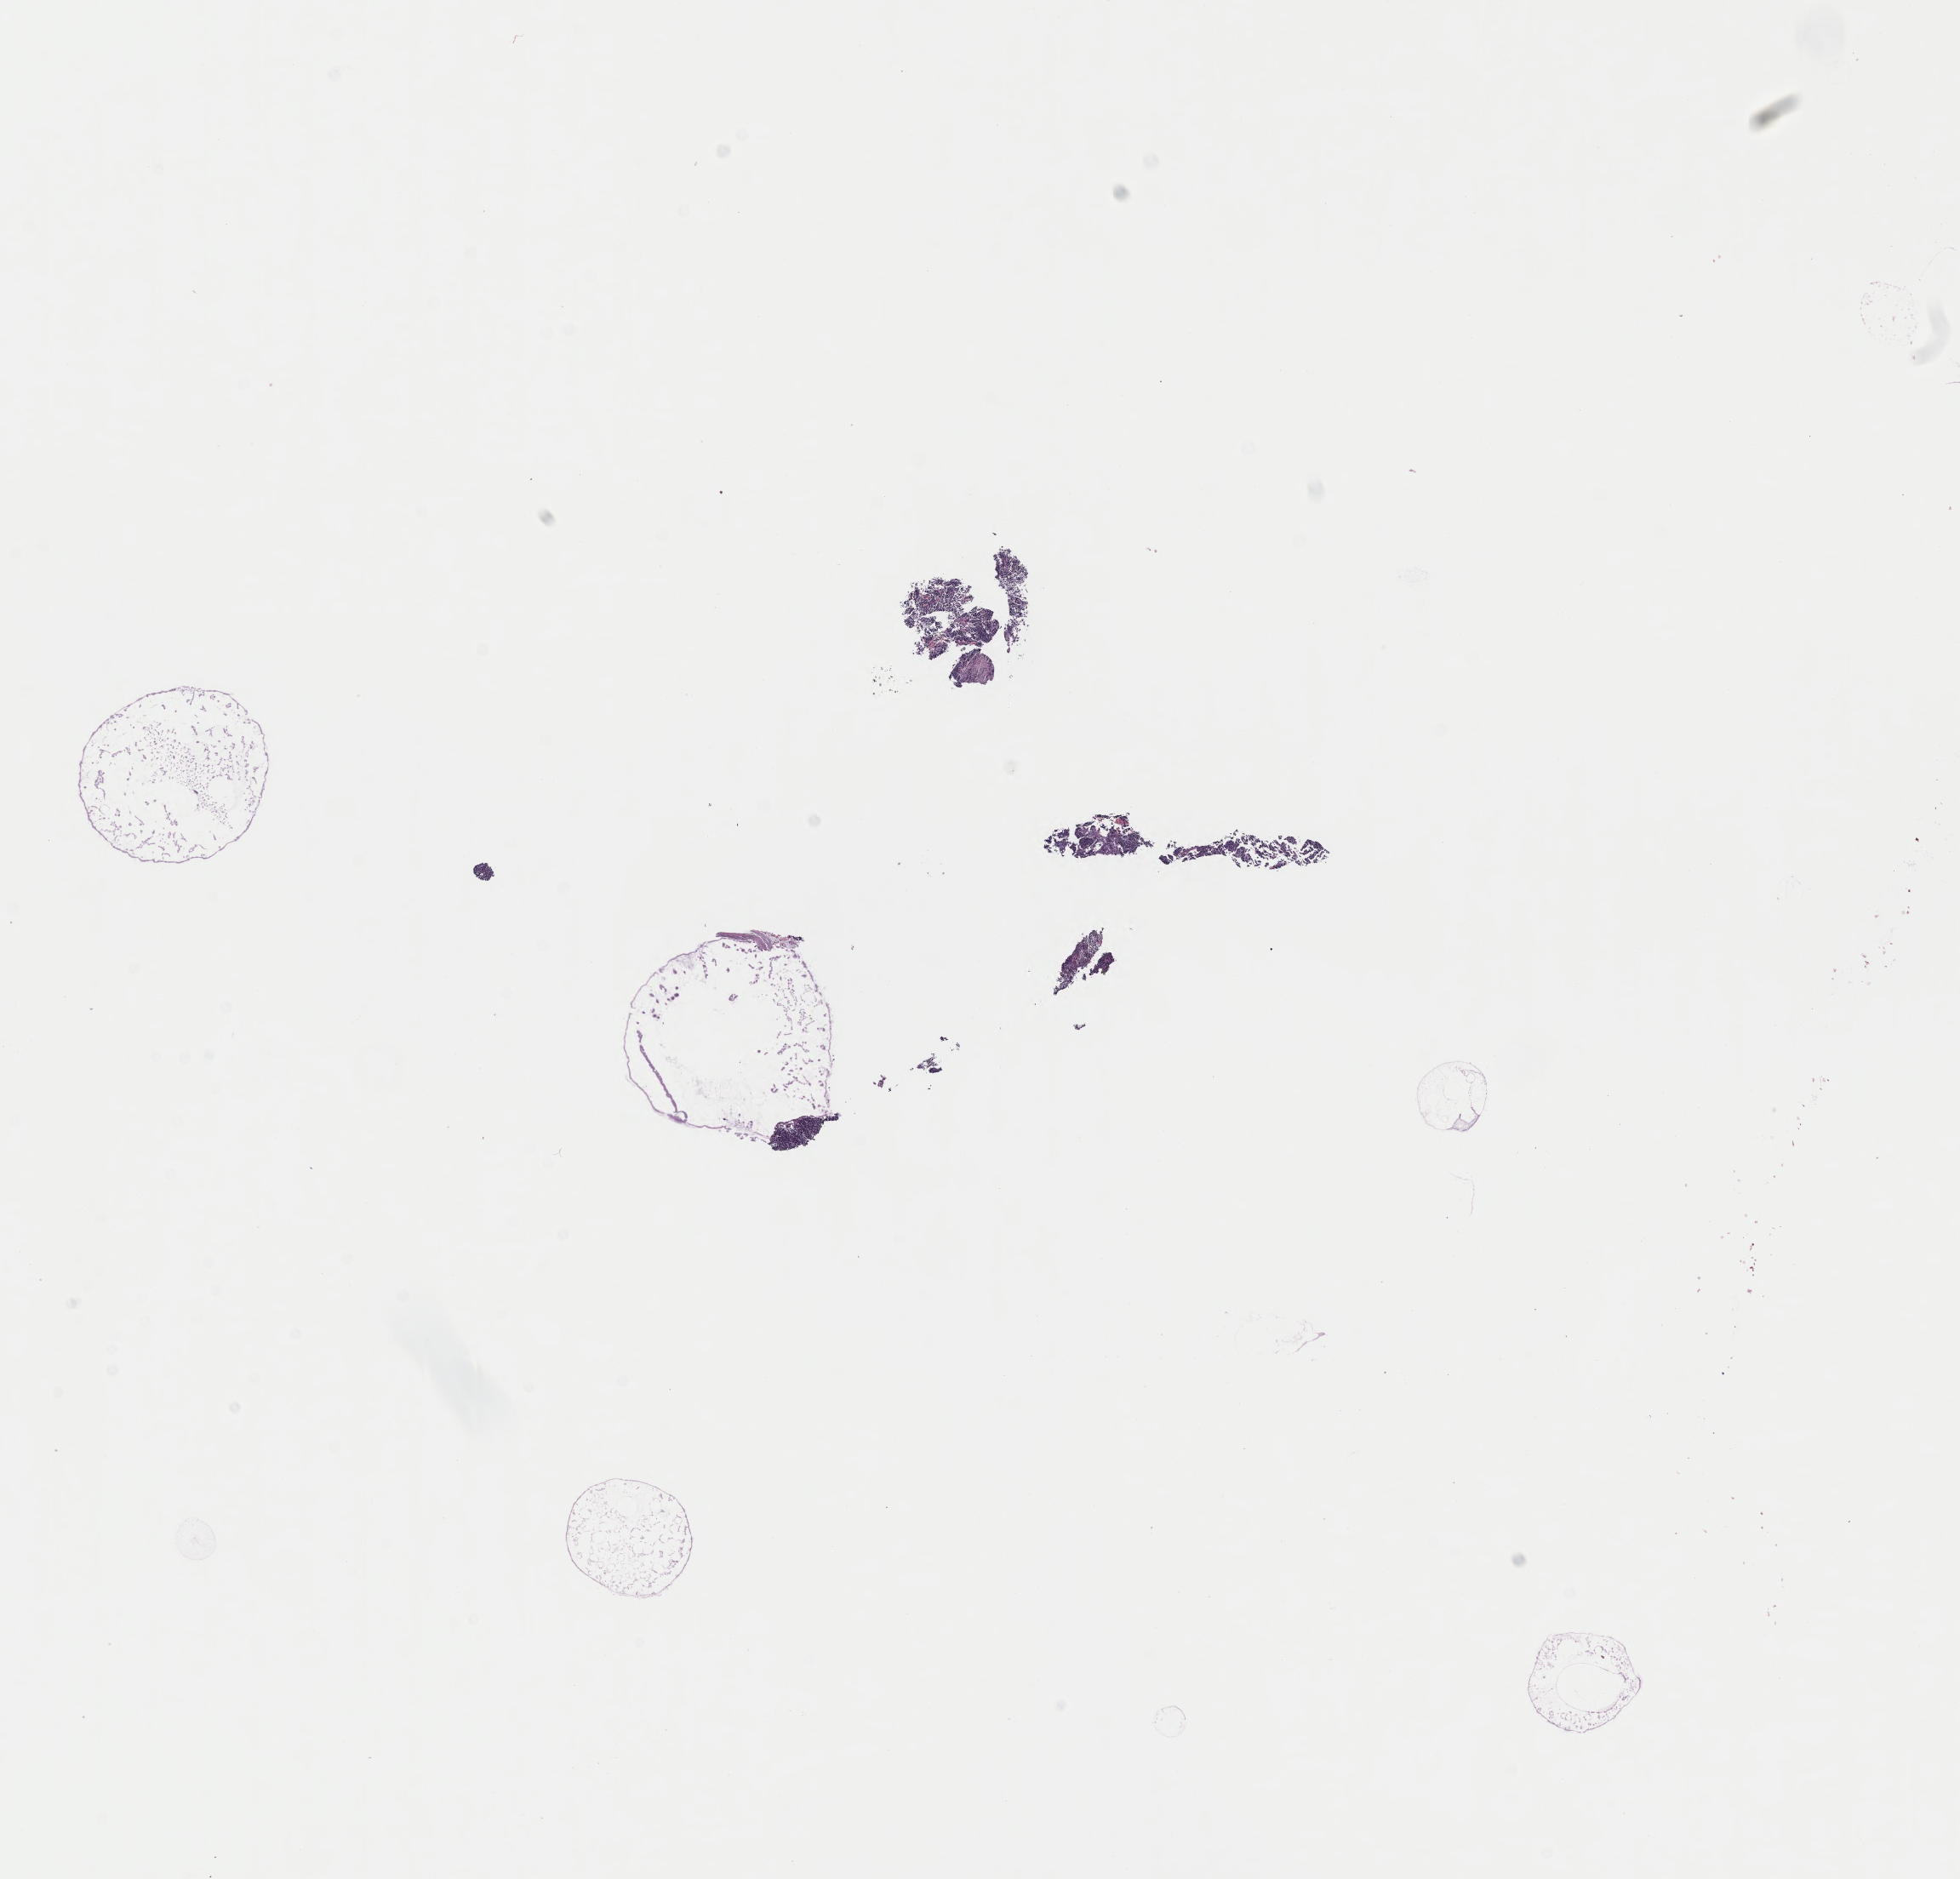
Haematoxylin and eosin whole-slide image of tumor tissue from the adrenal gland, whole scanned area (about 18.6 x 17.9 mm) shown as a low-resolution overview; FFPE section. Male patient, age 49 months (4 years 1 month).
Diagnosis (ICD-O-3 morphology term): Neuroblastoma, NOS.